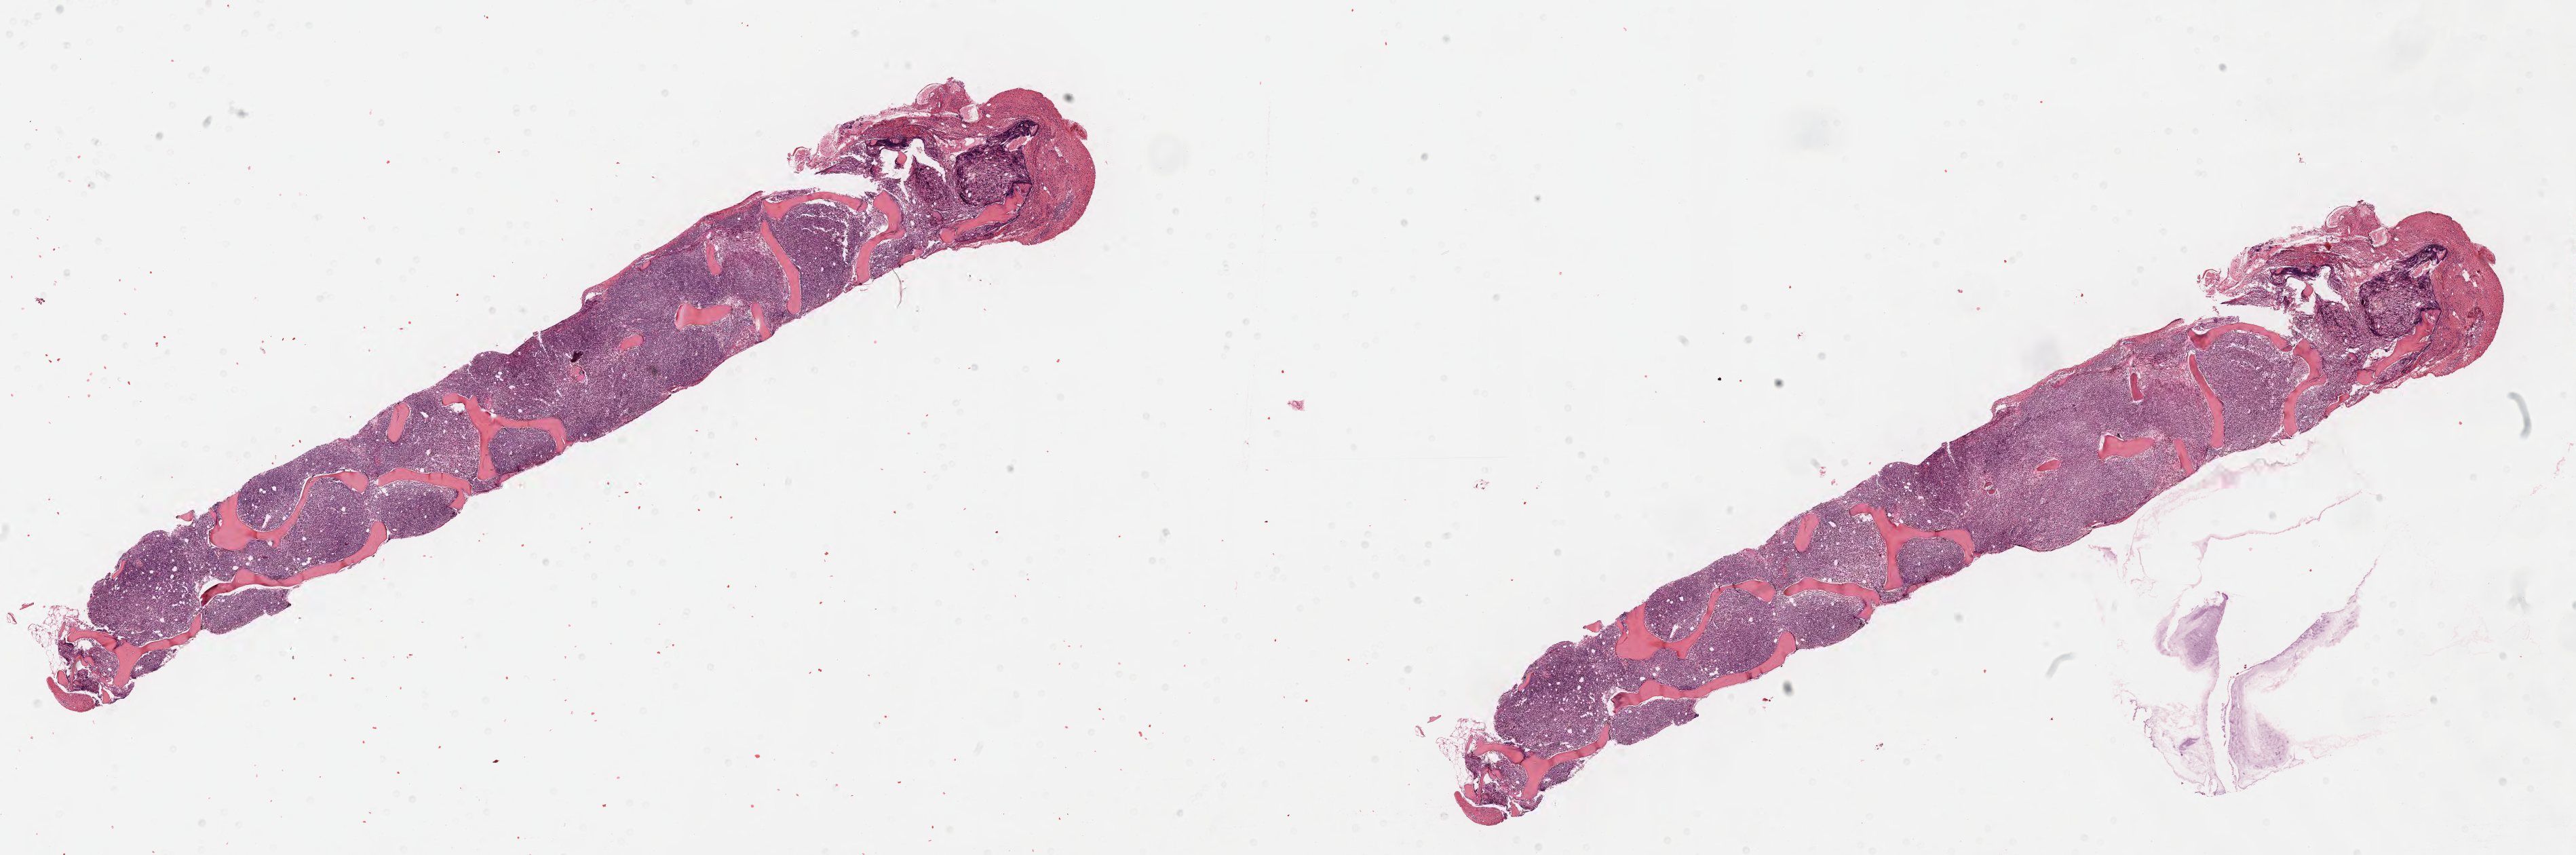
H&E whole-slide image, a low-resolution overview of the entire scanned area, about 30.7 x 10.2 mm, specimen: tumor tissue. Patient female; 64 years old.
- histologic diagnosis: Burkitt lymphoma, NOS